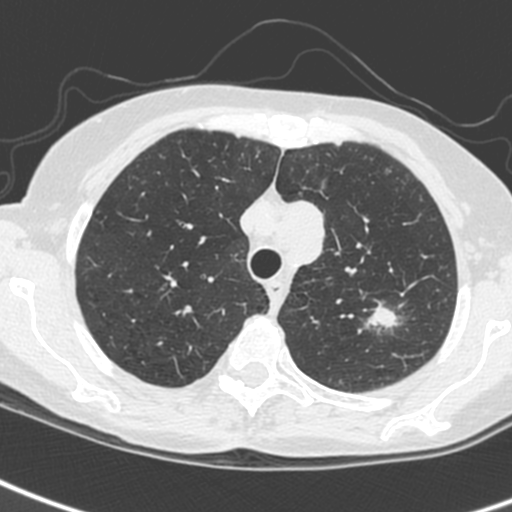
Axial slice from a low-dose chest CT screening exam. Baseline screening round. Lung window (W 1500 / L -600 HU). Standard (soft-tissue) reconstruction kernel (C). 120 kVp. Female, age 61 years at enrolment.
• Expert-annotated lung lesion, bounding box (x1, y1, x2, y2) in pixels: (347, 296, 411, 348).
• The screening reader recorded 2 non-calcified nodules or masses ≥4 mm on this exam; which of them this box marks is not recorded.
• Lung cancer was diagnosed 29 days after this screen: small cell carcinoma, NOS, left upper lobe, stage IV (AJCC 6th edition).